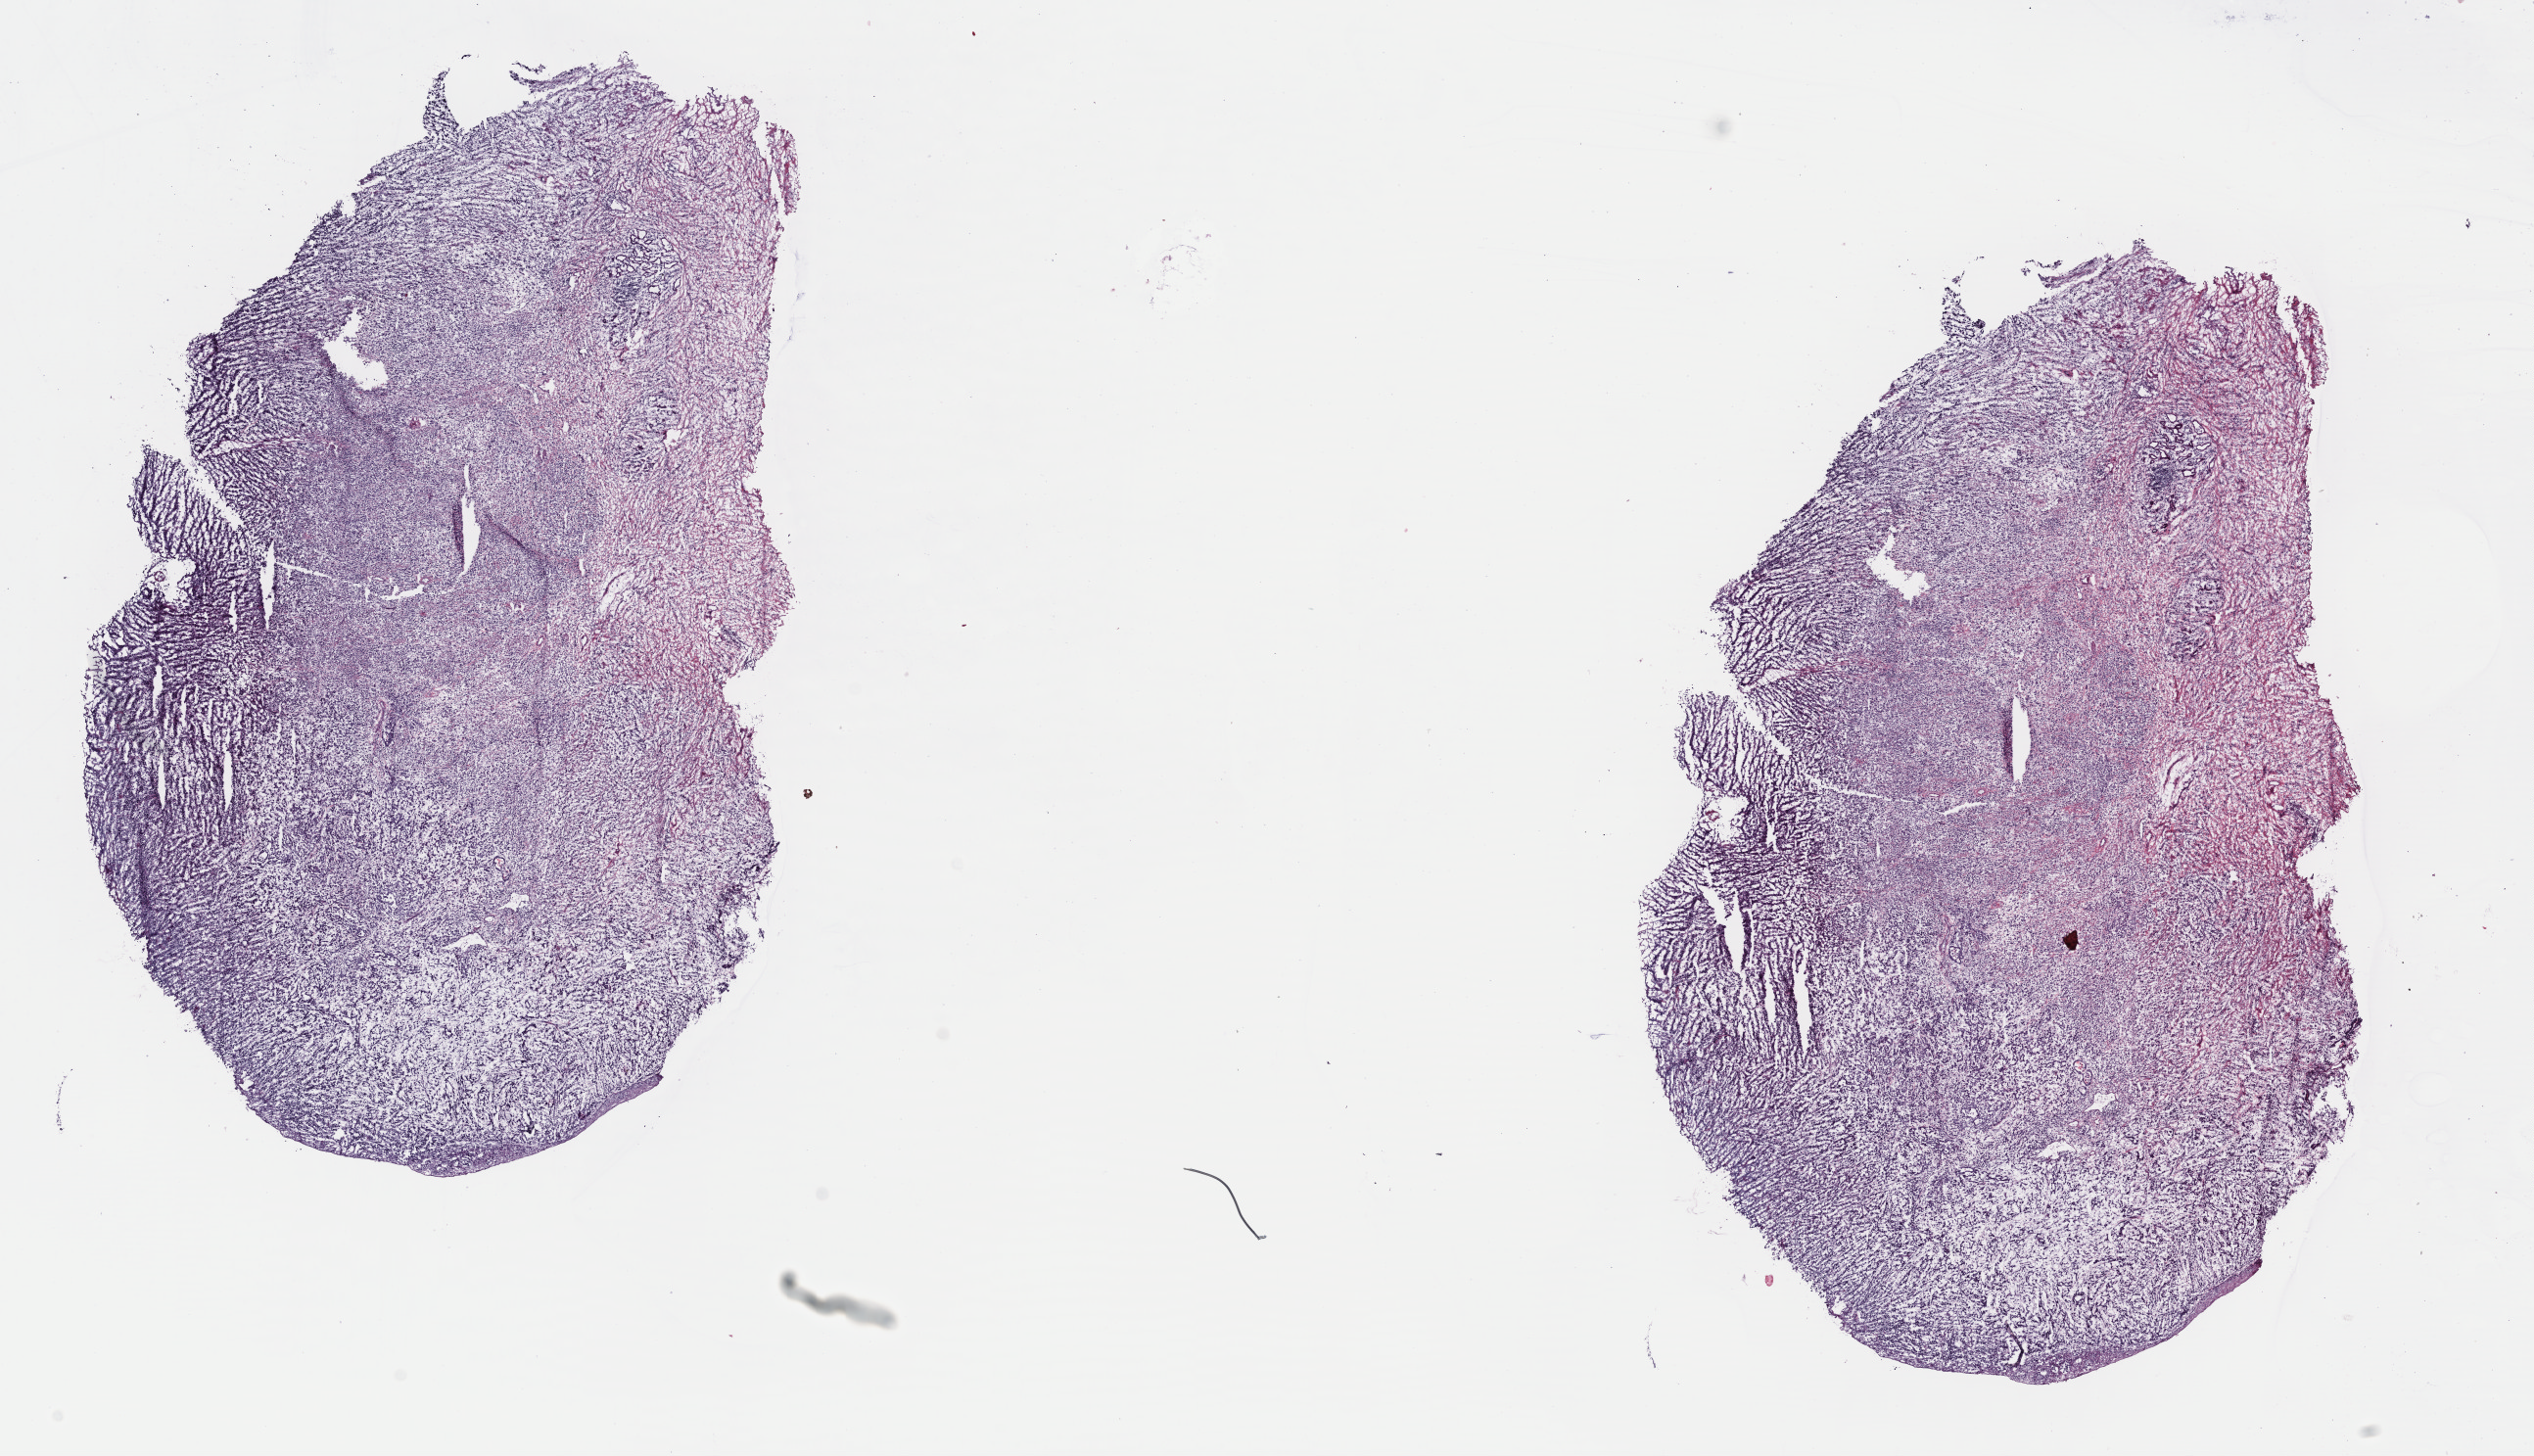
Whole-slide histology image, H&E — low-resolution overview of the scanned area, about 20.4 x 11.7 mm (from a 40x scan), frozen section from the top of the tissue portion, esophagus, primary tumour sample. Male, age 77 years at initial diagnosis. Histologic grade: GX (grade cannot be assessed). Slide review estimates, as recorded: tumour cells 100%, tumour nuclei 92%, normal cells 0%, stromal cells 0%, necrosis 0%. Infiltration values recorded for this section: lymphocyte infiltration 0%, monocyte infiltration 0%, neutrophil infiltration 0%.
AJCC pathologic stage: IV. Lymph nodes positive (case pathology): 6 of 11 examined. Histologic diagnosis: Adenocarcinoma, NOS (lower third of esophagus).